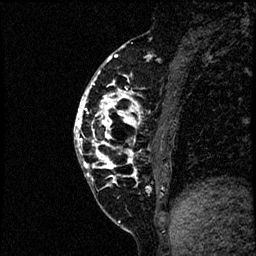
Breast MRI (dynamic contrast-enhanced), one sagittal slice; position 24 of 60 along the scan axis; dynamic contrast-enhanced study with each time point stored as its own series, time point 2 of 4 at this slice position (early post-contrast, ordered by acquisition time); 1.5 T; TE 4.2 ms, TR 17.6 ms; 2 mm slice thickness; 256 × 256 image matrix, field of view 200 × 200 mm. Patient: female, 40 years. Case-level facts recorded for this patient, not image findings: setting: breast cancer imaged before/during neoadjuvant chemotherapy; receptor status: HER2-positive.
Outlined on this slice (semi-automatically segmented with operator editing):
- analysis volume of interest (the breast-tissue region the enhancement analysis was run in; not a lesion): bounding box [x1, y1, x2, y2] px = [75, 56, 197, 205]
- tumour enhancement mask (voxels above the 100 % enhancement threshold inside the analysis volume of interest): [75, 56, 152, 190]